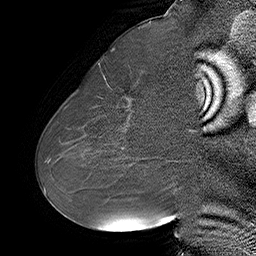
Breast MRI (dynamic contrast-enhanced), one sagittal slice; position 31 of 55 along the scan axis; dynamic contrast-enhanced series, time point 2 of 6 at this slice position (early post-contrast); 1.5 T; TE 4.5 ms, TR 32.4 ms; 256 × 256 image matrix, field of view 180 × 180 mm. Female patient. From the clinical record (not read from this slice): setting: breast cancer imaged before/during neoadjuvant chemotherapy; receptor status: HER2-positive.
Outlined on this slice (semi-automatically segmented with operator editing):
- analysis volume of interest (the breast-tissue region the enhancement analysis was run in; not a lesion): bounding box (x1, y1, x2, y2) in pixels: (80, 64, 163, 134)
- tumour enhancement mask (voxels above the 100 % enhancement threshold inside the analysis volume of interest): (128, 99, 130, 101)